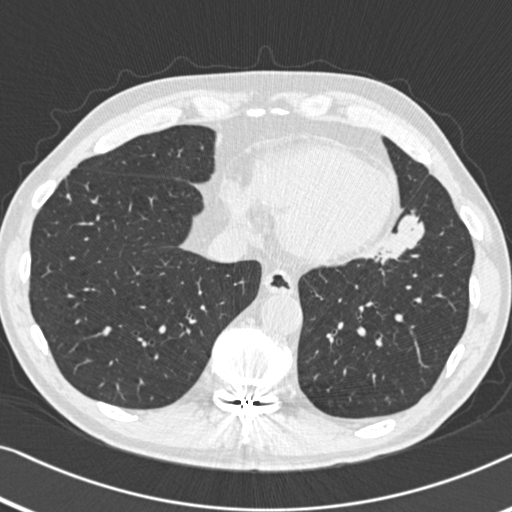
Low-dose screening chest CT, one axial slice; position 134 of 383 along the scan axis; reconstruction kernel B30f; 120 kVp; lung window (W 1500 / L -600 HU); 512 × 512 image matrix.
Structures marked on this image (outlined manually by an expert reader):
- lesion 1 (tumor, upper lobe of left lung): bounding box <378,214,425,264> (left, top, right, bottom; pixels)